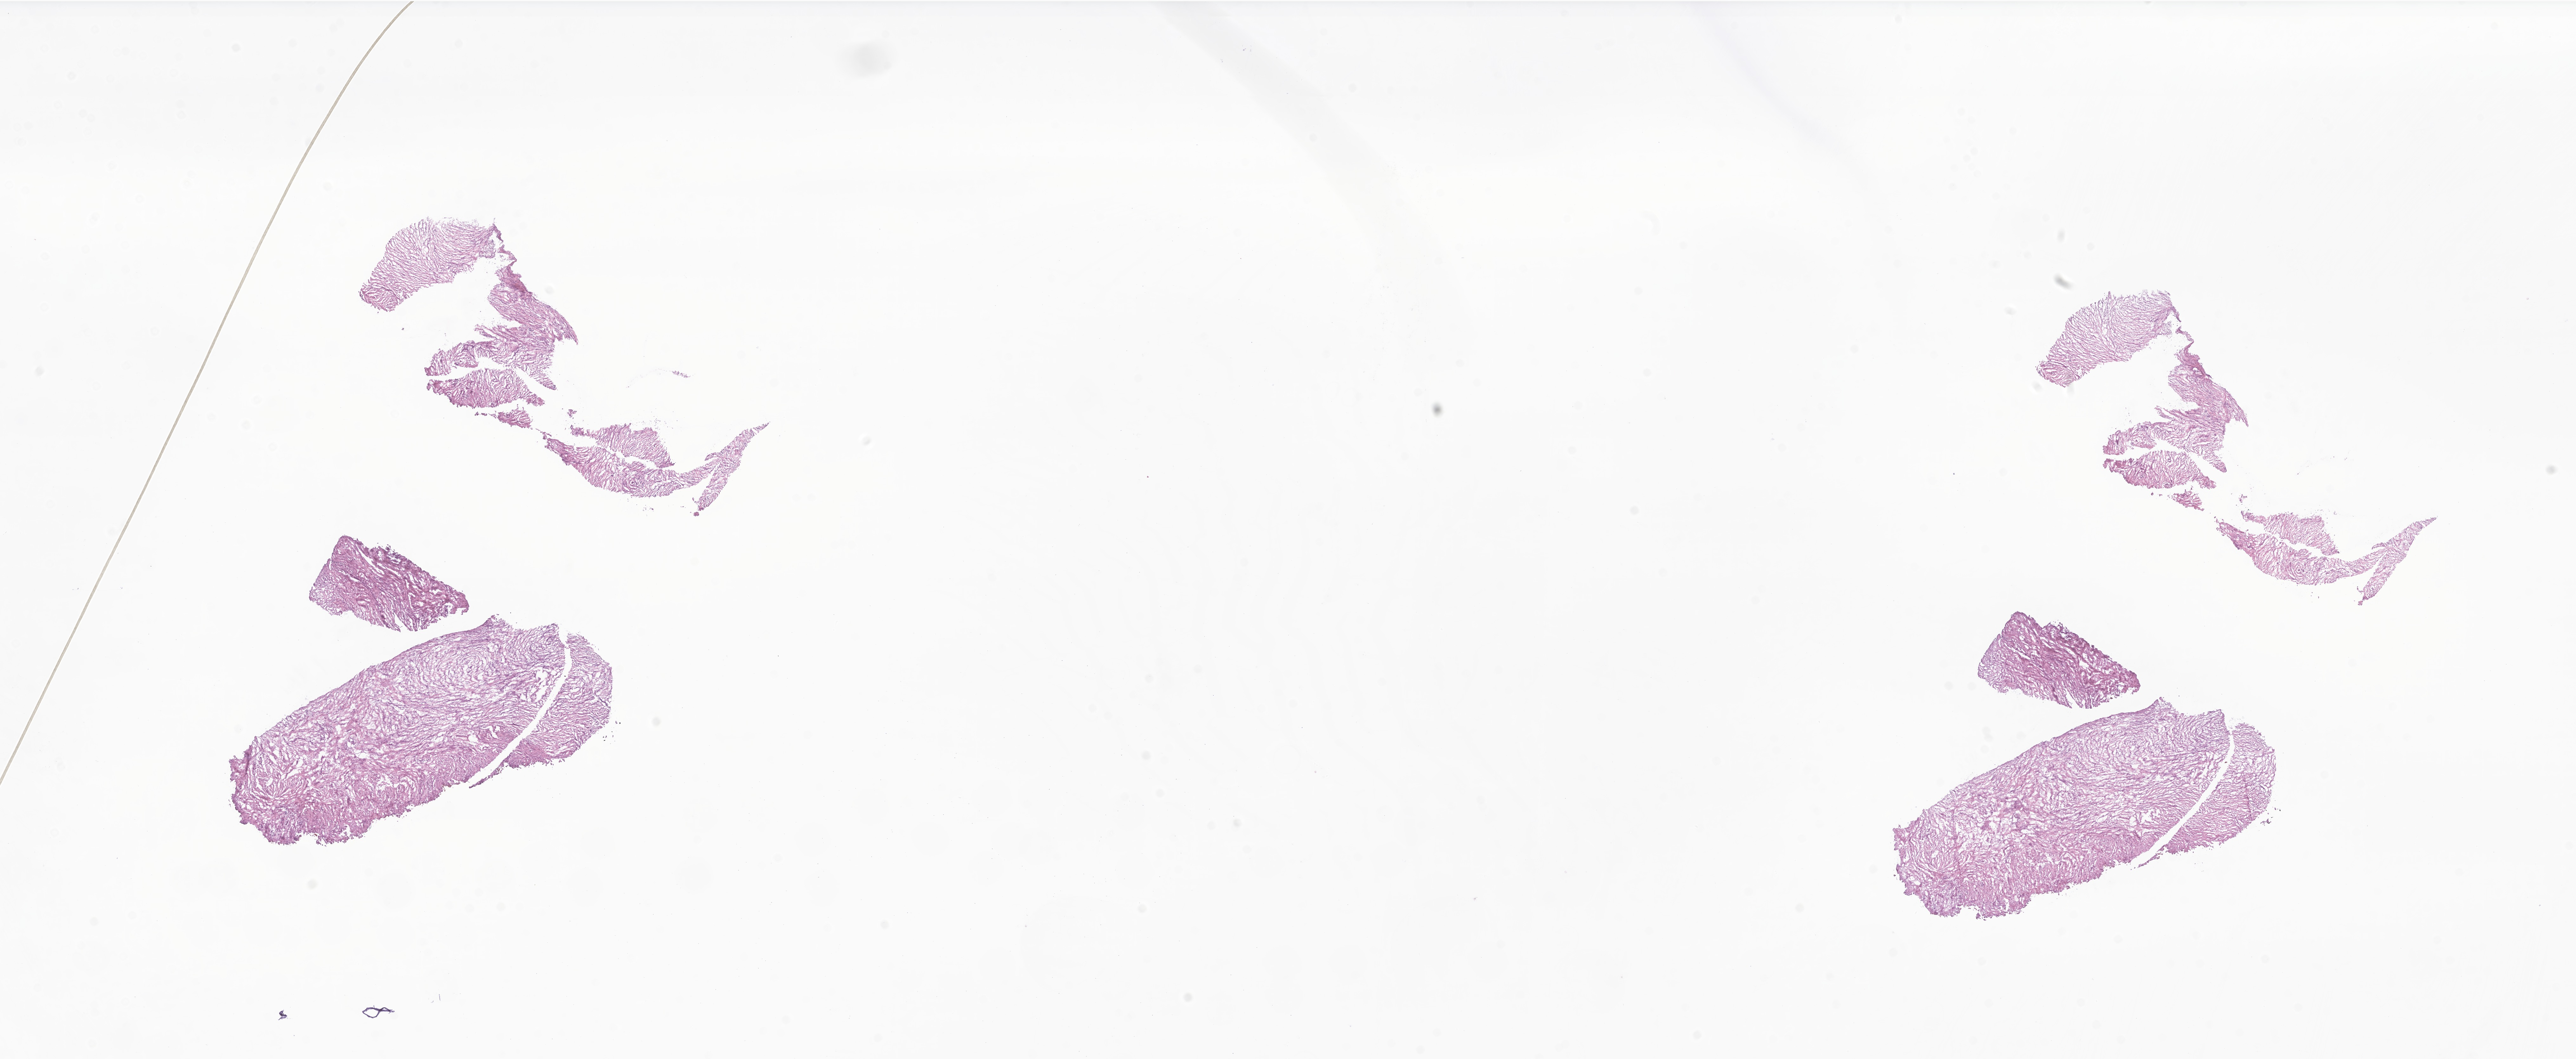
Haematoxylin and eosin whole-slide image of tumor tissue from the brain, shown as a low-resolution overview of the whole scanned area (about 34.2 x 14.1 mm), frozen section. Male patient, age 36 months (3 years).
• recorded diagnosis: Pleomorphic xanthoastrocytoma, NOS